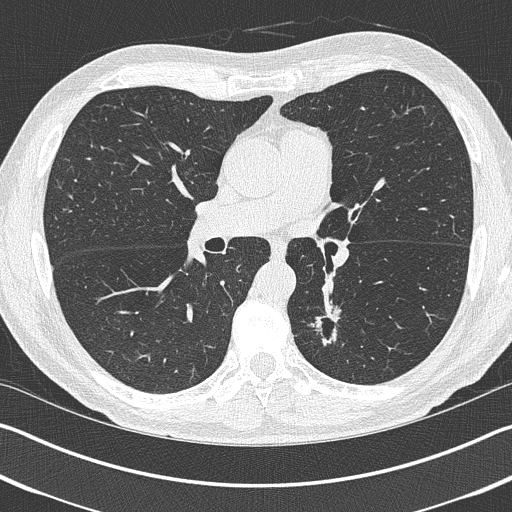
Low-dose screening chest CT, axial slice; baseline screening round; lung window (W 1500 / L -600 HU); 1 mm slice thickness; slice 173 of 402 in the series. Male participant, aged 69 years at enrolment. Current smoker at enrolment.
- Lesion marked by an expert reader, box from (x=295, y=305) to (x=351, y=362) px.
- The exam's reader record, not a measurement of the box and not confirmed to be the same lesion: non-calcified nodule or mass ≥4 mm, left upper lobe, 19 × 19 mm, spiculated (stellate) margins, pre-existing on the prior screen: yes.
- Official screen result: positive, change unspecified: nodule(s) >= 4 mm or enlarging nodule(s), mass(es), or other non-specific abnormalities suspicious for lung cancer.
- Participant outcome: lung cancer diagnosed 202 days after this screen — non-small cell carcinoma, left lower lobe, stage IIIA (AJCC 6th edition), 20 mm at pathology.